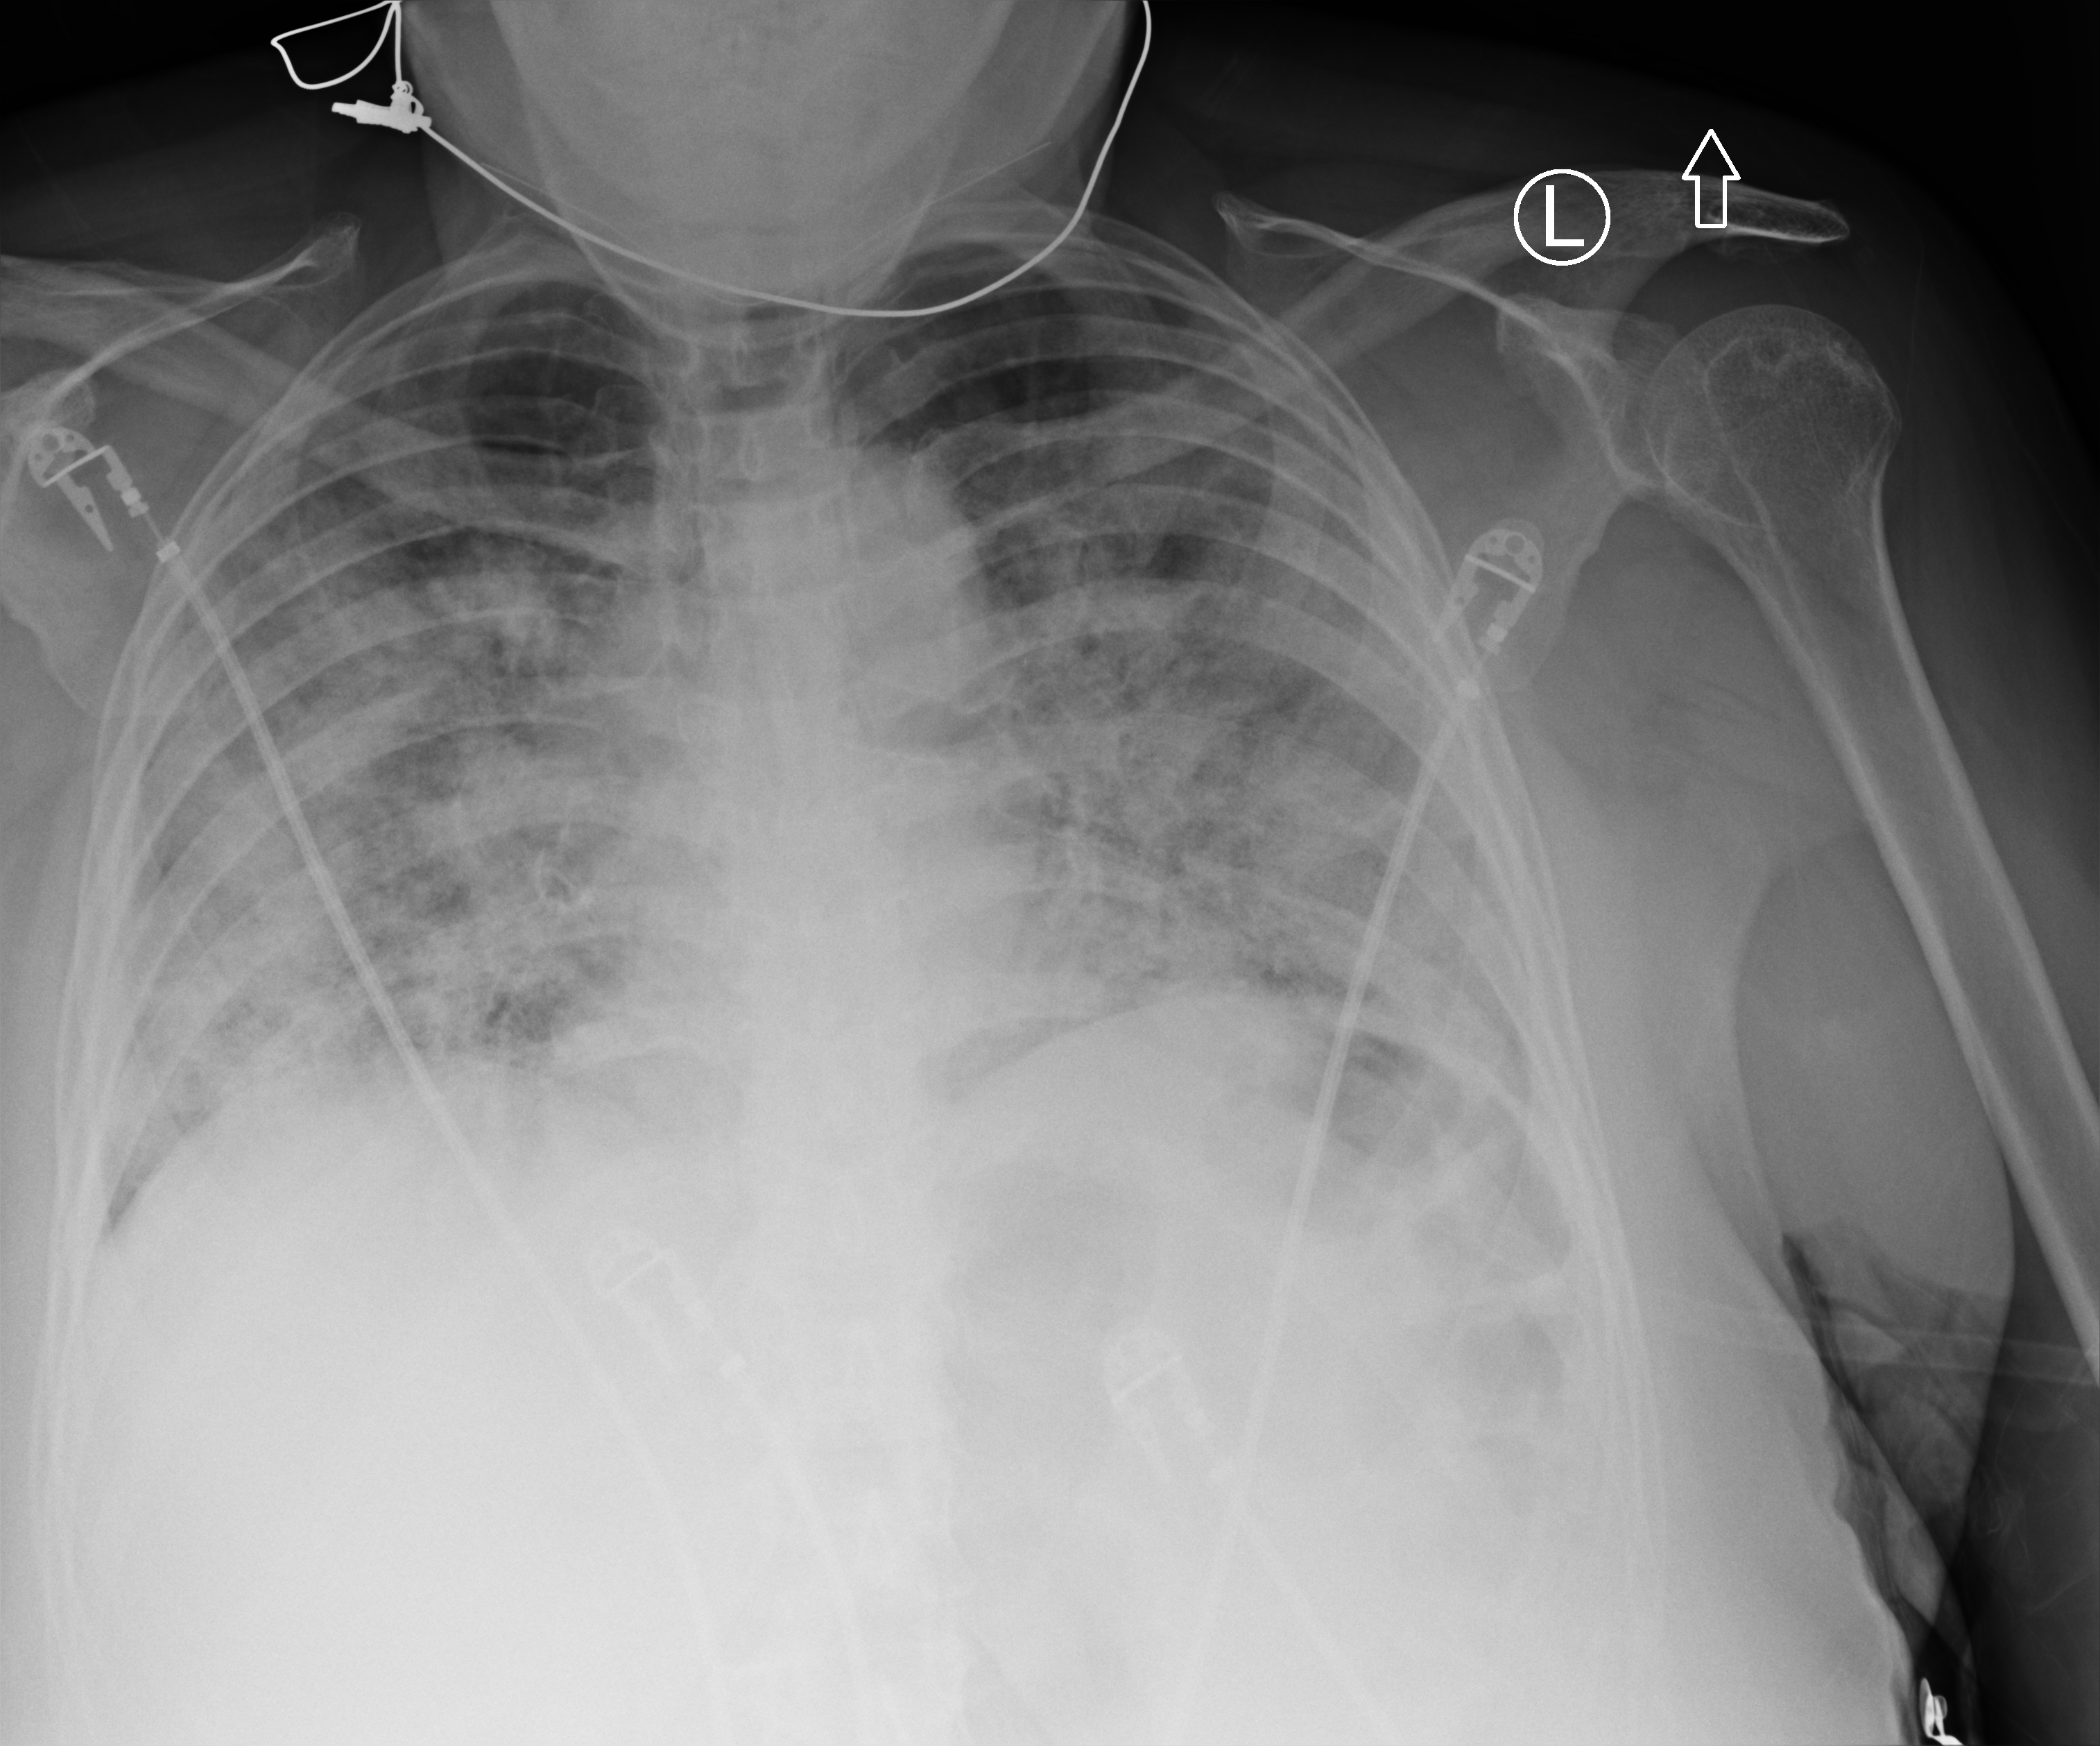
Portable chest radiograph. Patient hospitalised with COVID-19; female, aged 75–90 years.
Admission-level facts for this patient (not findings on this image; timing relative to this image not recorded):
- length of hospital stay: 26 days
- mechanically ventilated during this hospital stay: yes